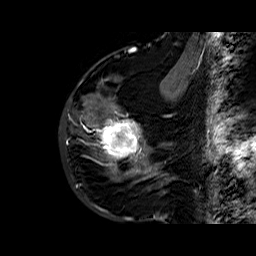
Breast MRI (dynamic contrast-enhanced), one sagittal slice; dynamic contrast-enhanced series, time point 2 of 6 at this slice position (early post-contrast); 1.5 T; TE 6.4 ms, TR 32.8 ms; 4 mm slice thickness; 256 × 256 image matrix. Female patient. Case-level facts recorded for this patient, not image findings: setting: breast cancer imaged before/during neoadjuvant chemotherapy; receptor status: HR-positive, HER2-negative.
Annotated regions visible in this slice (semi-automatic segmentation, software-assisted and operator-edited):
- analysis volume of interest (the breast-tissue region the enhancement analysis was run in; not a lesion): bounding box <86,77,163,177> (left, top, right, bottom; pixels)
- tumour enhancement mask (voxels above the 100 % enhancement threshold inside the analysis volume of interest): <94,110,157,176>